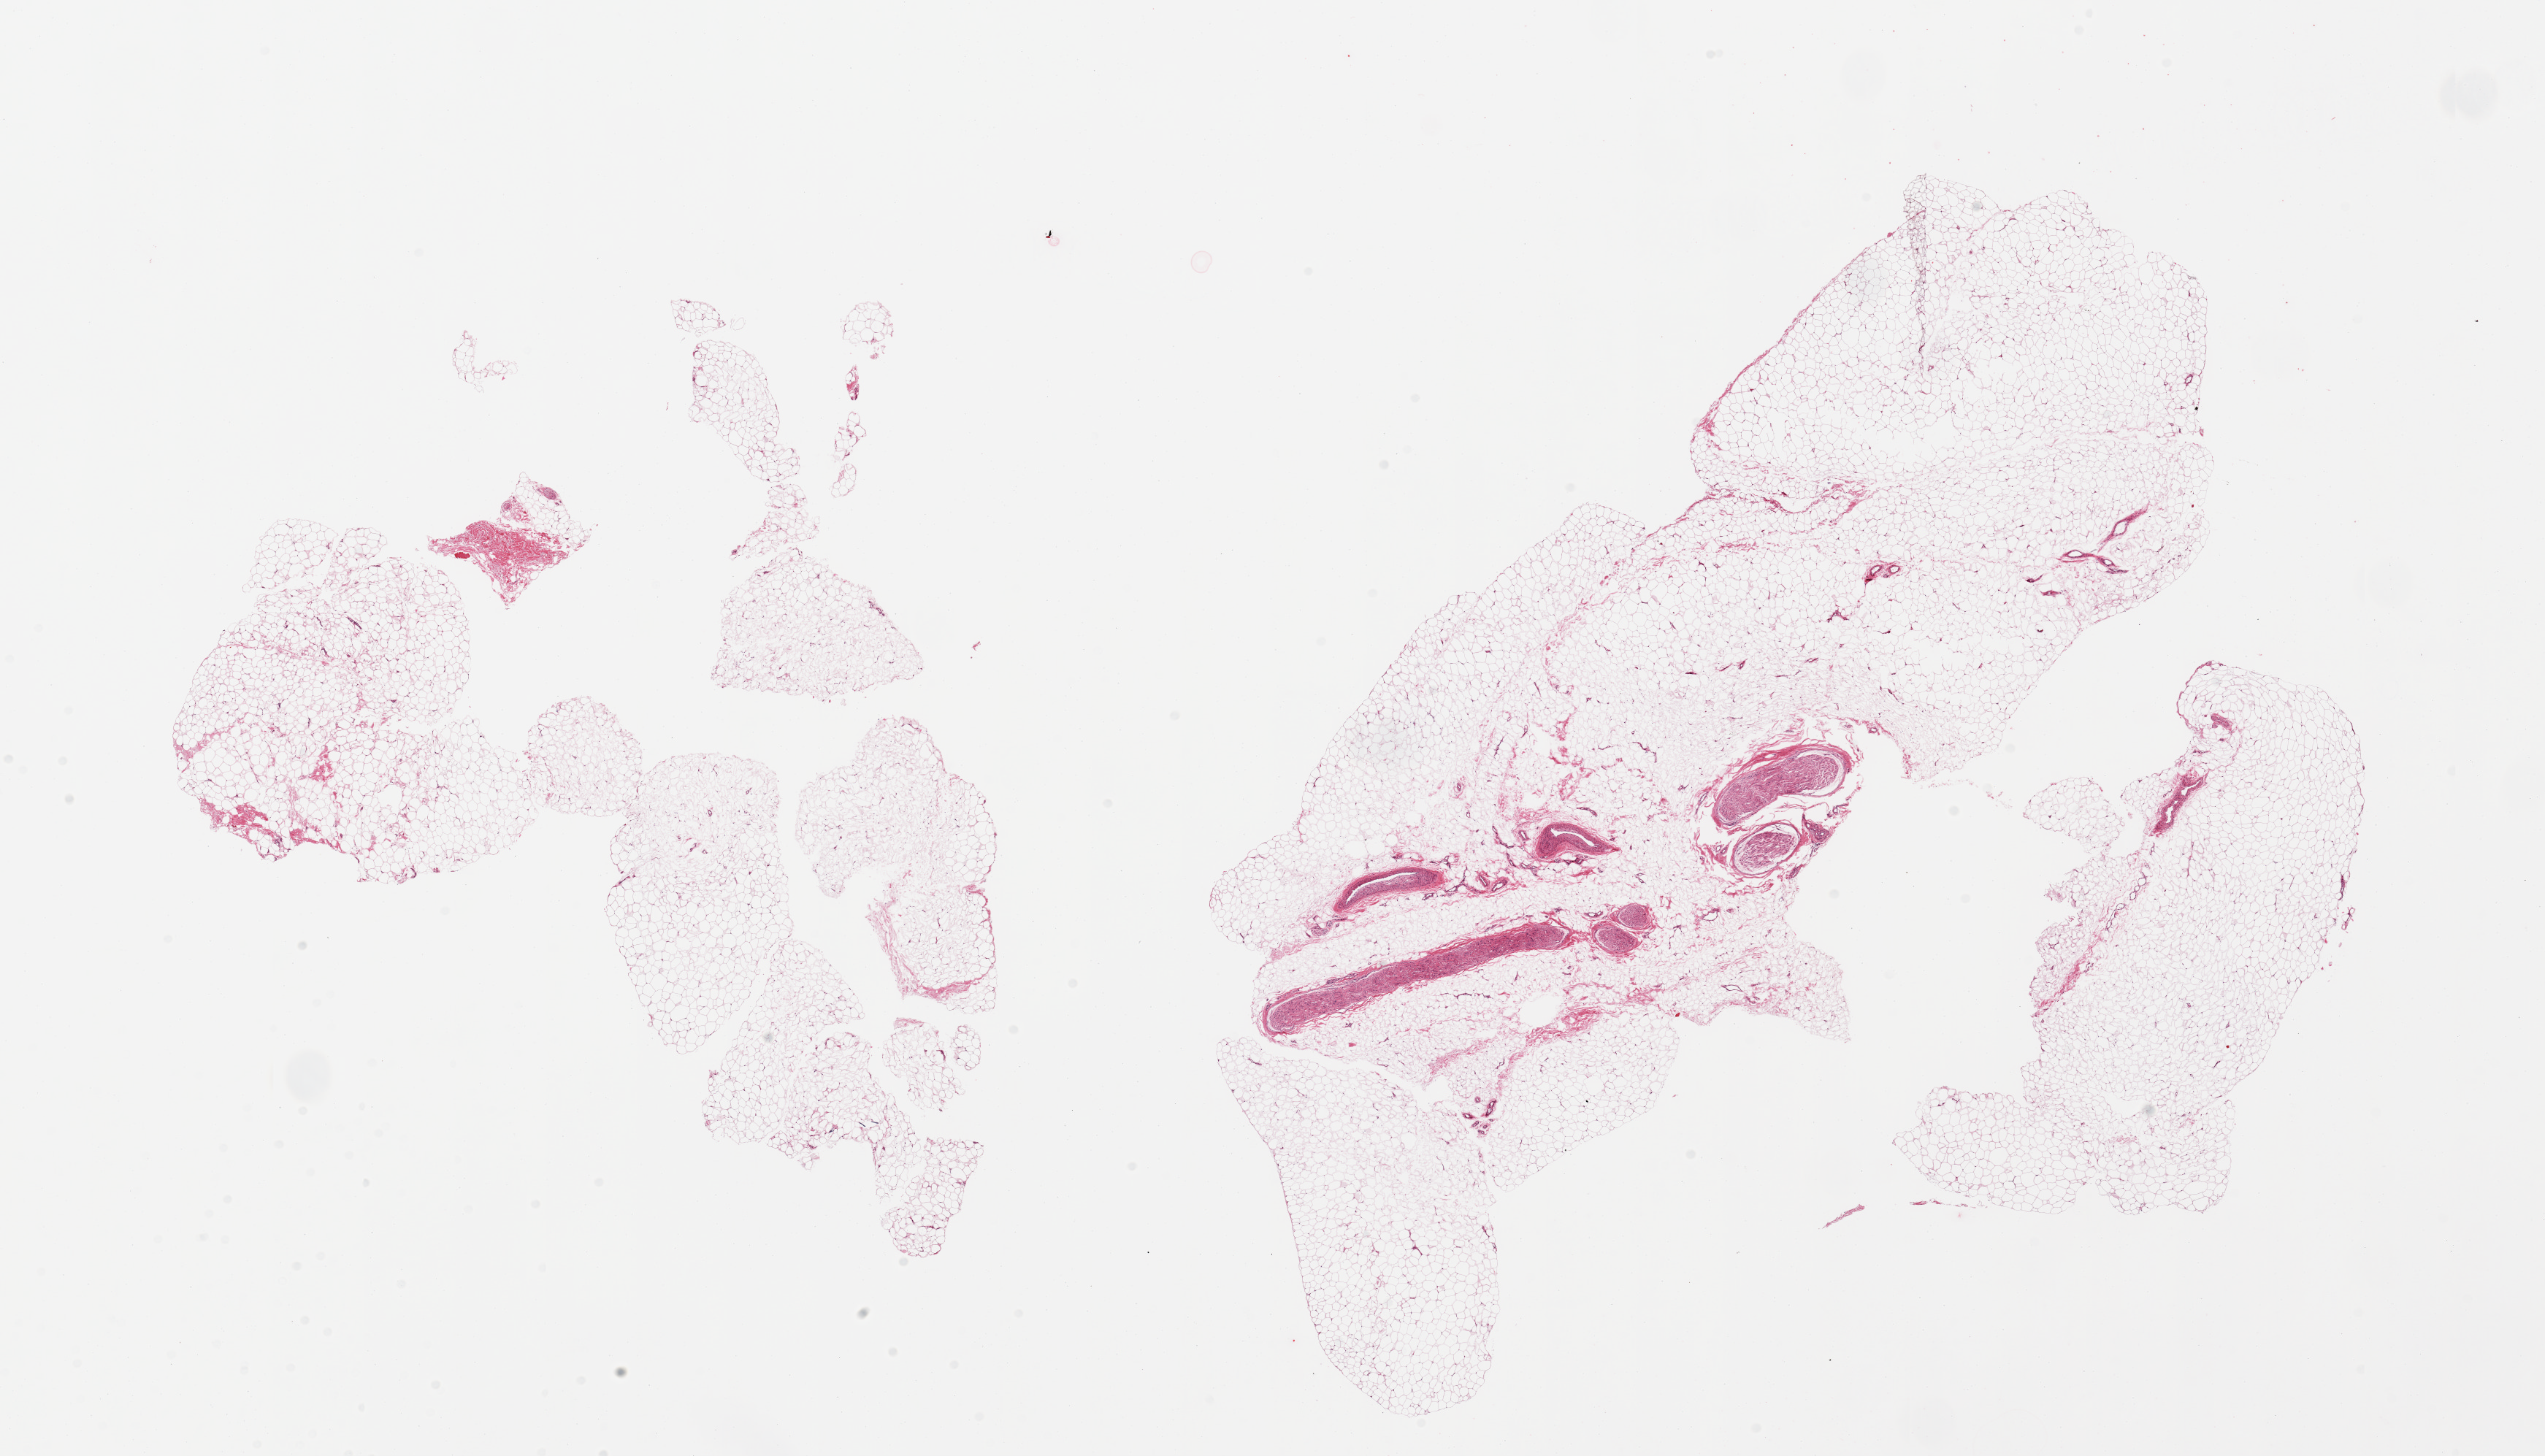
Digitized H&E-stained section, brightfield — low-resolution overview of the scanned area, about 27.6 x 15.8 mm (slide scanned at 20x), PAXgene-fixed, paraffin-embedded tissue, target tissue: adipose tissue, donor tissue sample. Donor sex: male.
Review note (as recorded): 2 pieces, ~incidental peripheral nerve embedded.